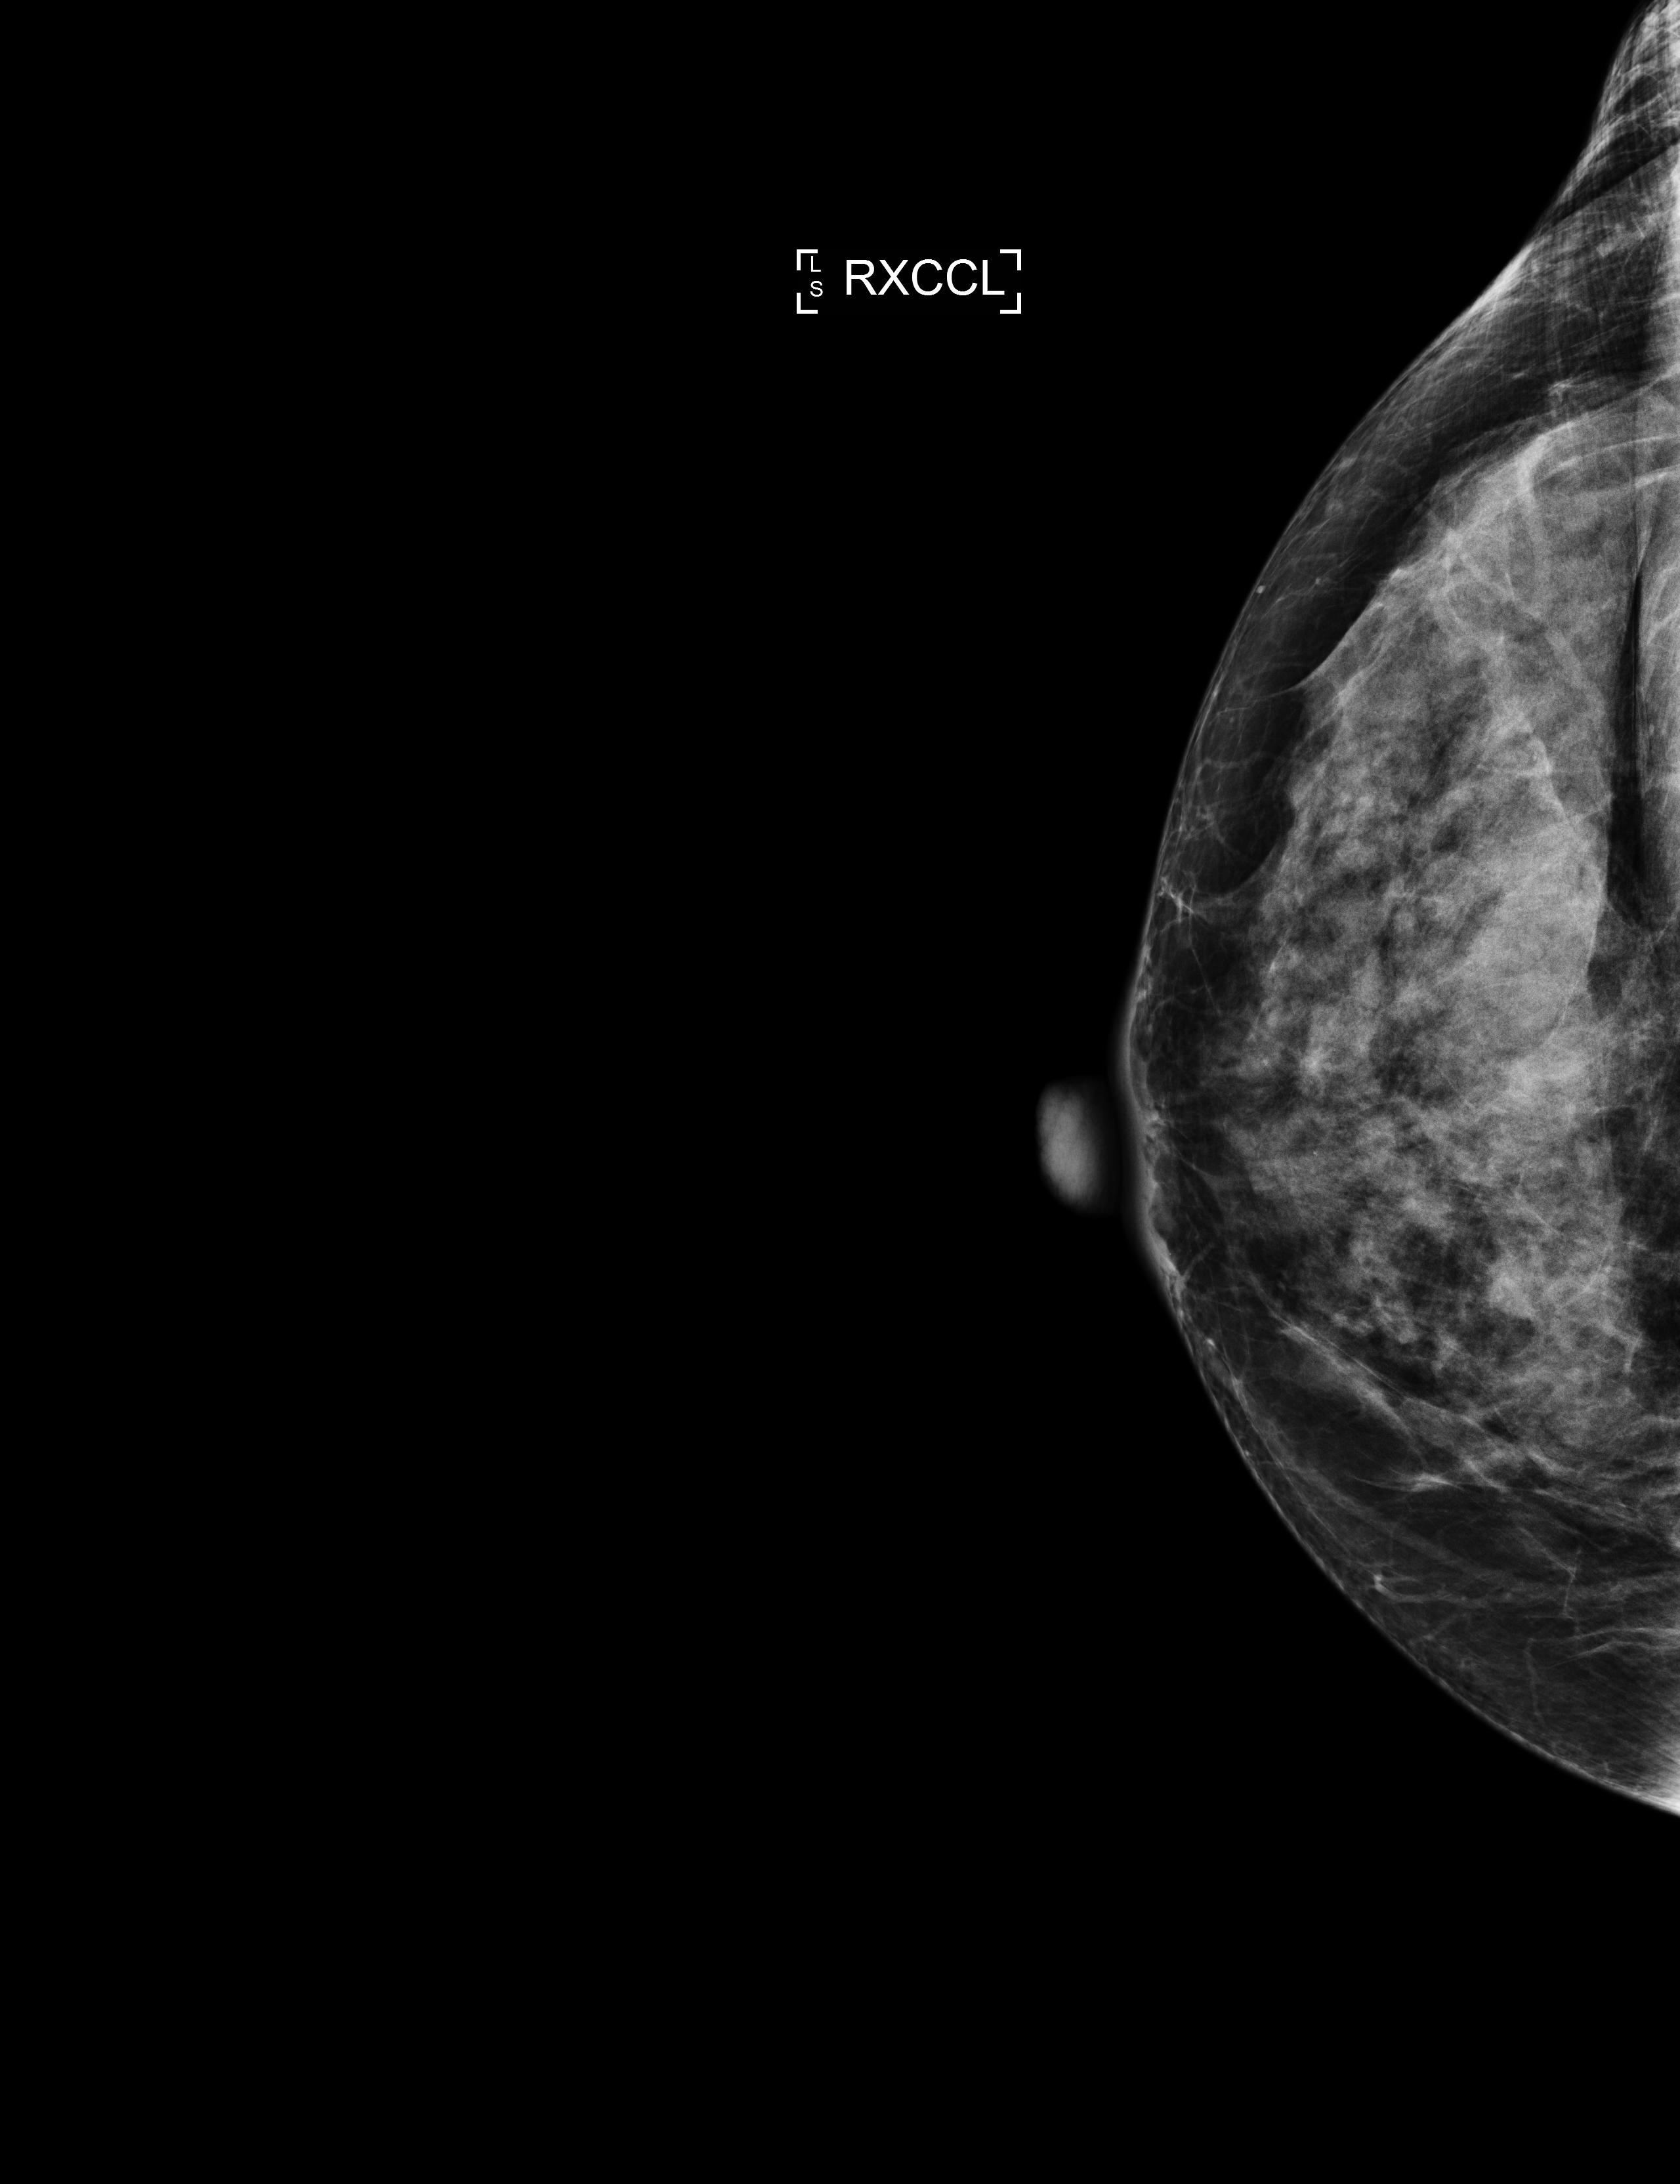
Annual screening mammography examination, compressed breast thickness 51 mm, system: Selenia Dimensions. Female patient, age 68 years.
Image type: full-field digital mammogram. Breast: right. Projection: exaggerated CC view (lateral).